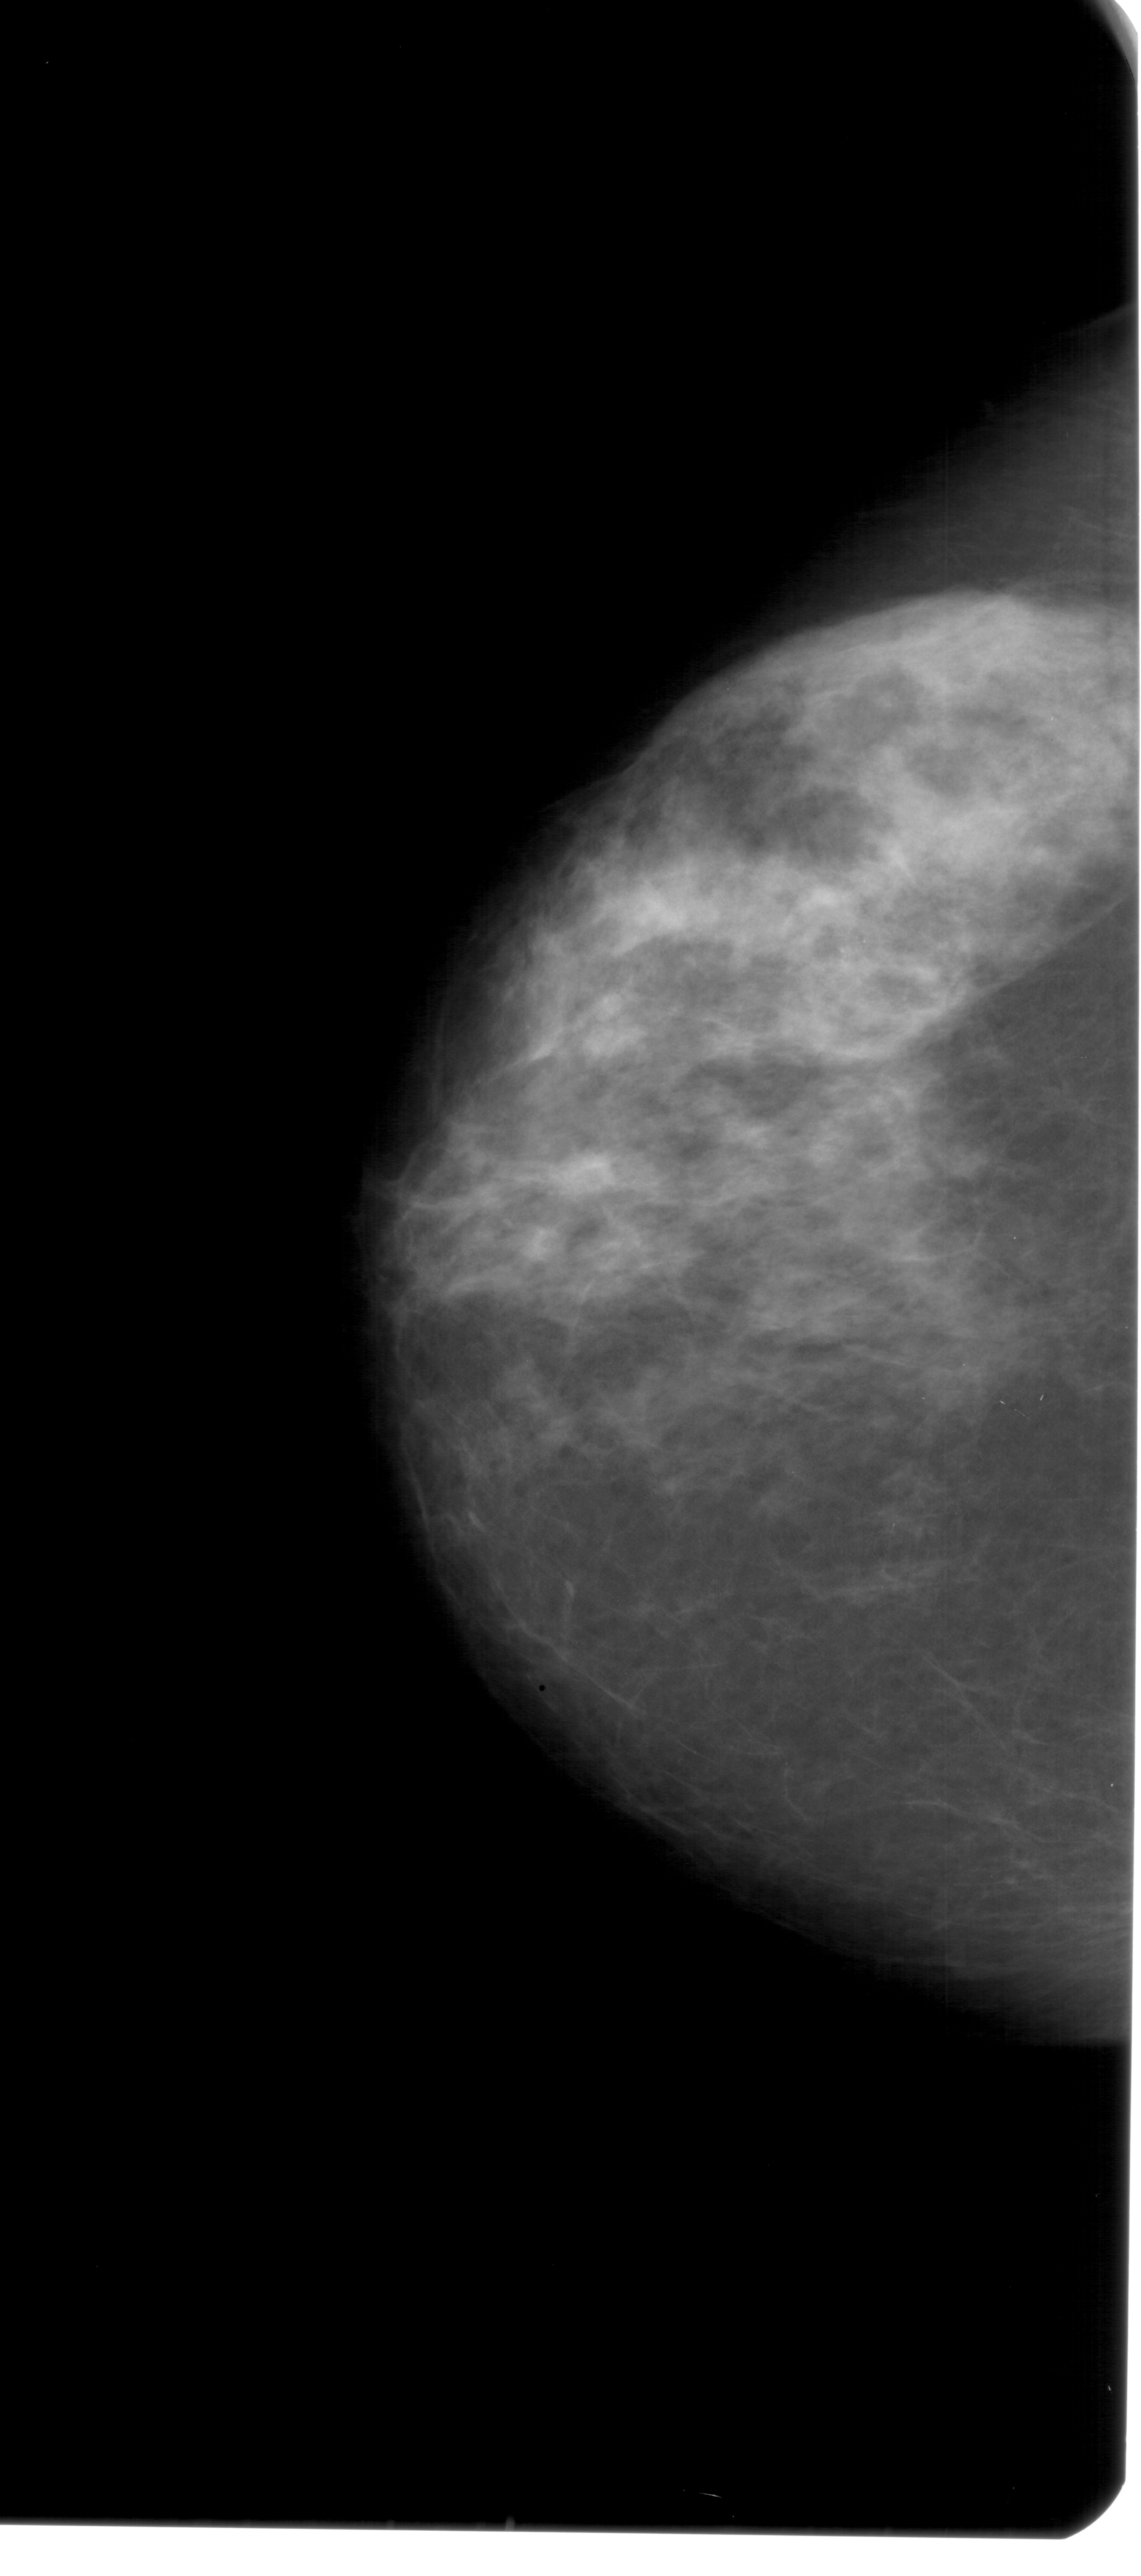
Mammogram (digitized film). Left breast. Craniocaudal (CC) view. Breast composition: heterogeneously dense (BI-RADS density category 3 of 4). 1141 × 2576 image matrix.
Expert-marked regions of interest on this film, with their recorded descriptors:
- calcifications, morphology pleomorphic, distribution clustered; BI-RADS assessment category 4; subtlety rating 2 on a 1 (subtle) to 5 (obvious) scale; pathology result (as recorded, not read from the image): benign: bounding box [x1, y1, x2, y2] px = [817, 928, 882, 981]